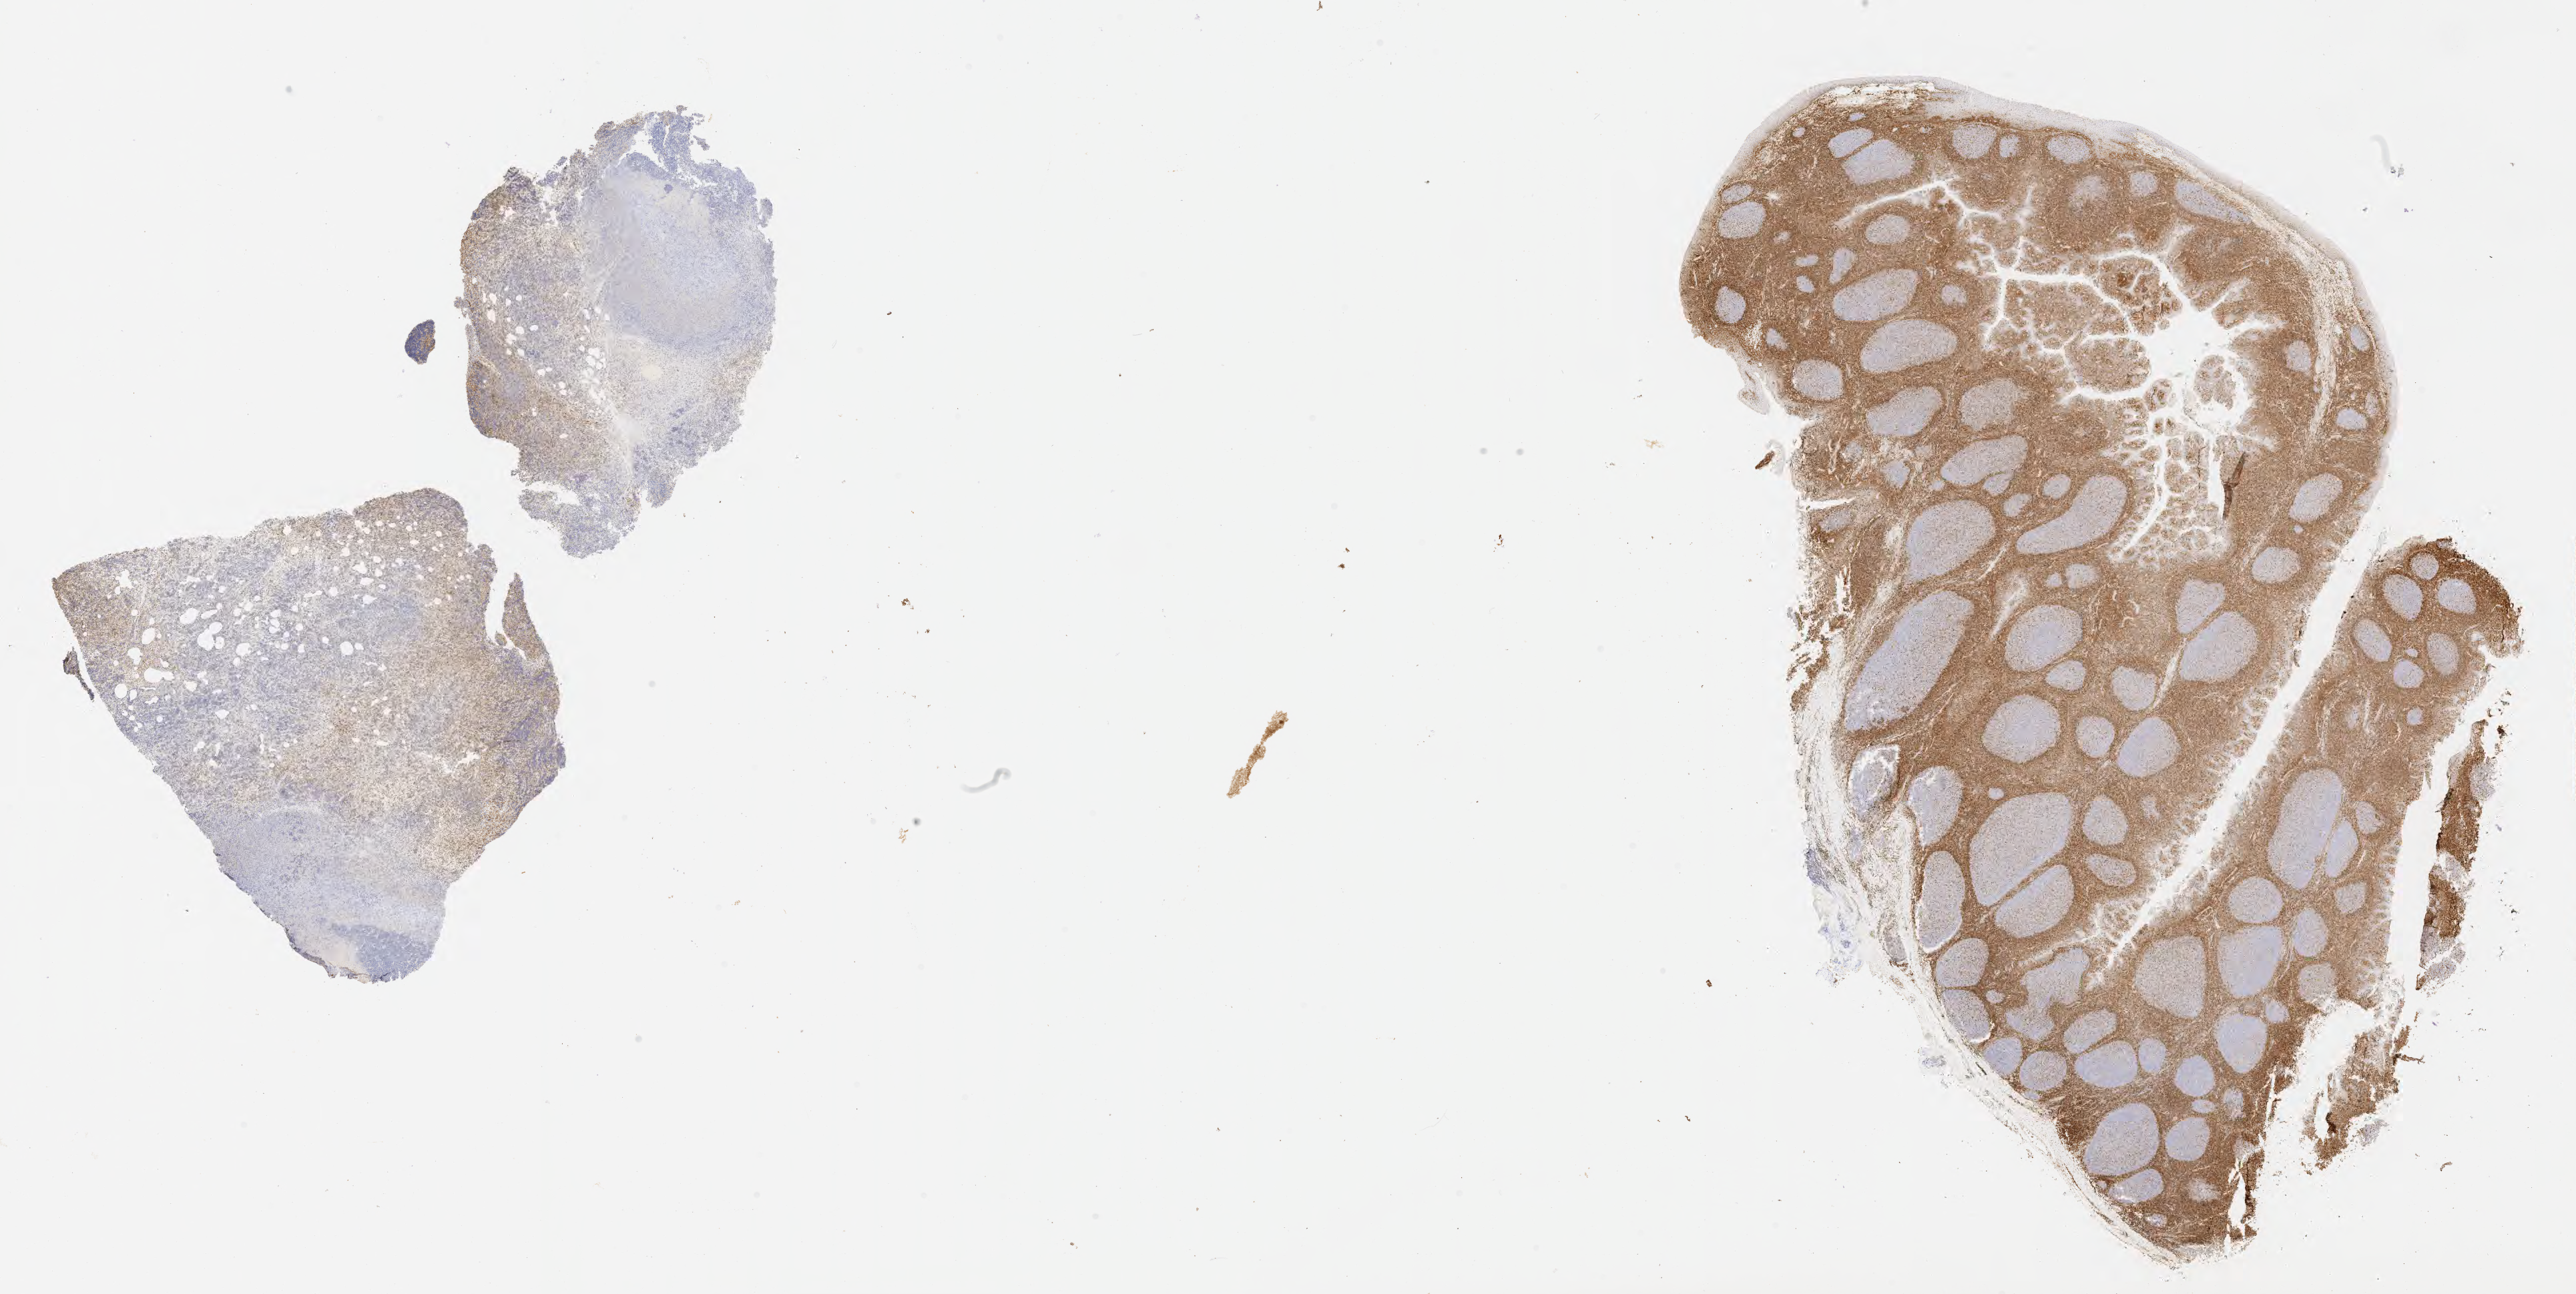
Whole-slide image, immunohistochemical stain for BCL2, shown as a low-resolution overview of the whole scanned area (about 31.2 x 15.7 mm); tumor tissue; anatomic site: mandible. Patient: male, age at initial diagnosis 7 years.
Histologic diagnosis: Burkitt lymphoma, NOS.